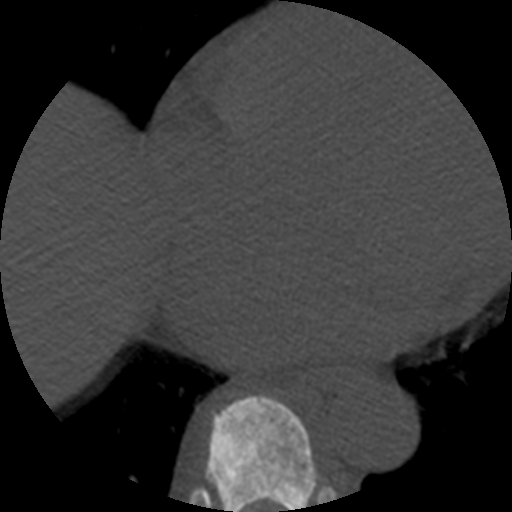
CT including the spine, one axial slice; position 315 of 508 along the scan axis; 120 kVp; bone window (W 1800 / L 400 HU); 512 × 512 image matrix, field of view 160 × 160 mm. Patient age 57 years. From the clinical record (not read from this slice): primary cancer: prostate.
Outlined on this slice (semi-automatically segmented with operator editing):
- T8 vertebra: bounding box <206,394,318,512> (left, top, right, bottom; pixels)